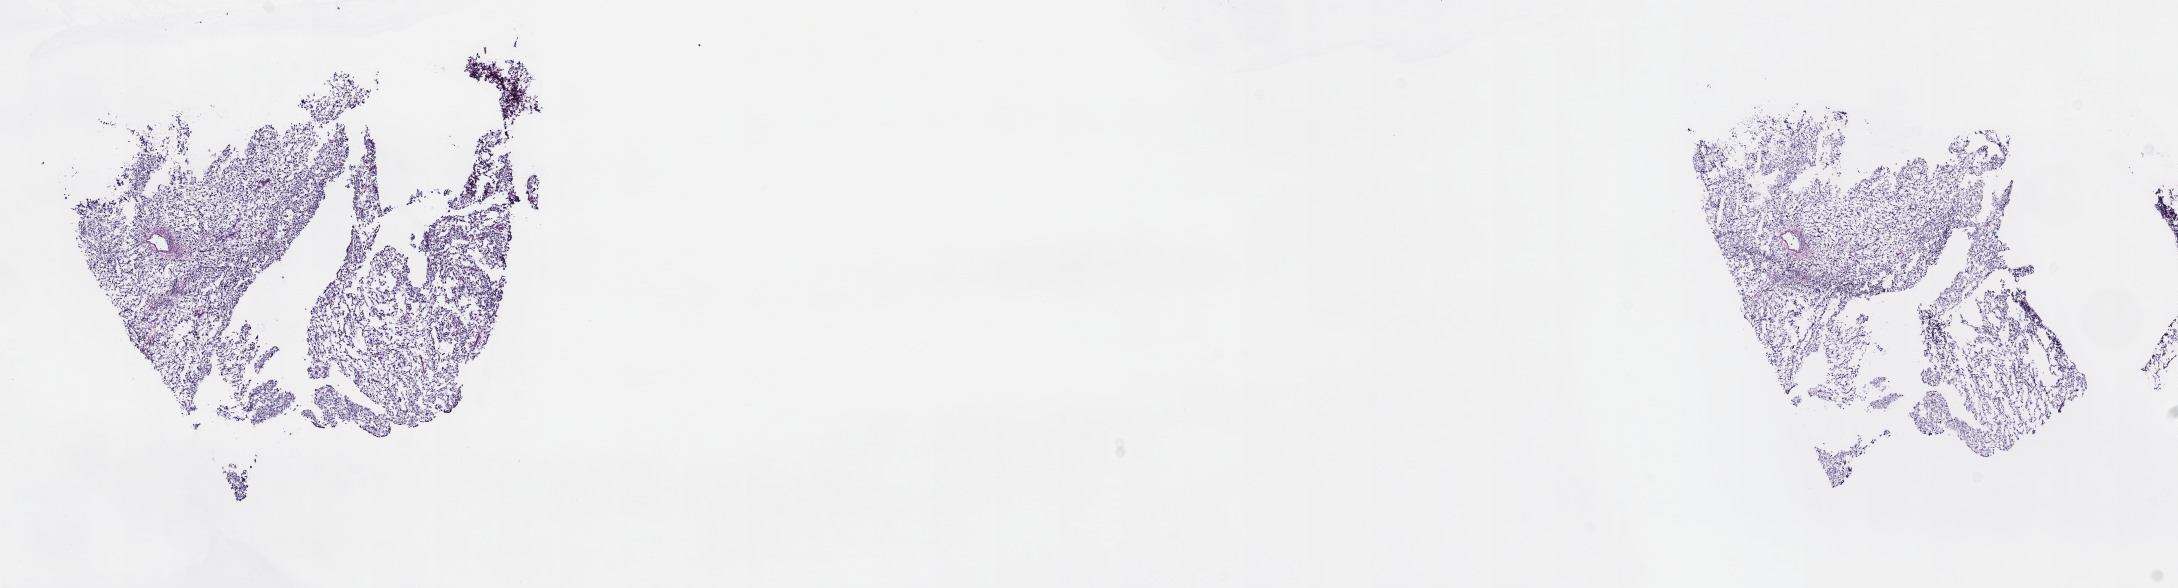
Digitized H&E-stained tissue section (whole slide) — low-resolution overview of the scanned area, about 17.6 x 4.8 mm (acquisition: 40x scan), frozen section from the top of the tissue portion, primary tumour sample from the connective, subcutaneous and other soft tissues. Female, age 59 years at initial diagnosis. Pathologist review of this section (percent, as recorded): tumour cells 100%, tumour nuclei 80%, normal cells 0%, stromal cells 0%, necrosis 0%. Infiltration values recorded for this section: lymphocyte infiltration 4%, monocyte infiltration 0%, neutrophil infiltration 0%.
• pathologic diagnosis: Fibromyxosarcoma (connective, subcutaneous and other soft tissues of lower limb and hip)